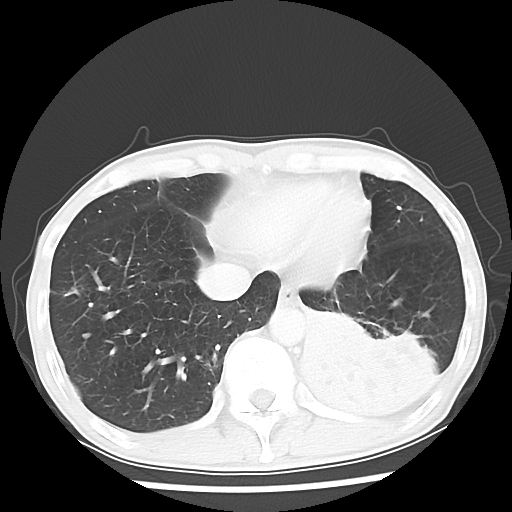
Chest CT, one axial slice. Position 14 of 64 along the scan axis. Lung window (W 1500 / L -600 HU). 5 mm slice thickness. 512 × 512 image matrix, field of view 313 × 313 mm. Male patient, age 68 years. From the clinical record (not read from this slice): clinical TNM (as recorded): T4 N0 M0.
Annotated regions visible in this slice (rectangle marked by the reading radiologist):
- lung tumour (recorded histology: squamous cell carcinoma): bounding box [x1, y1, x2, y2] px = [287, 300, 441, 412]